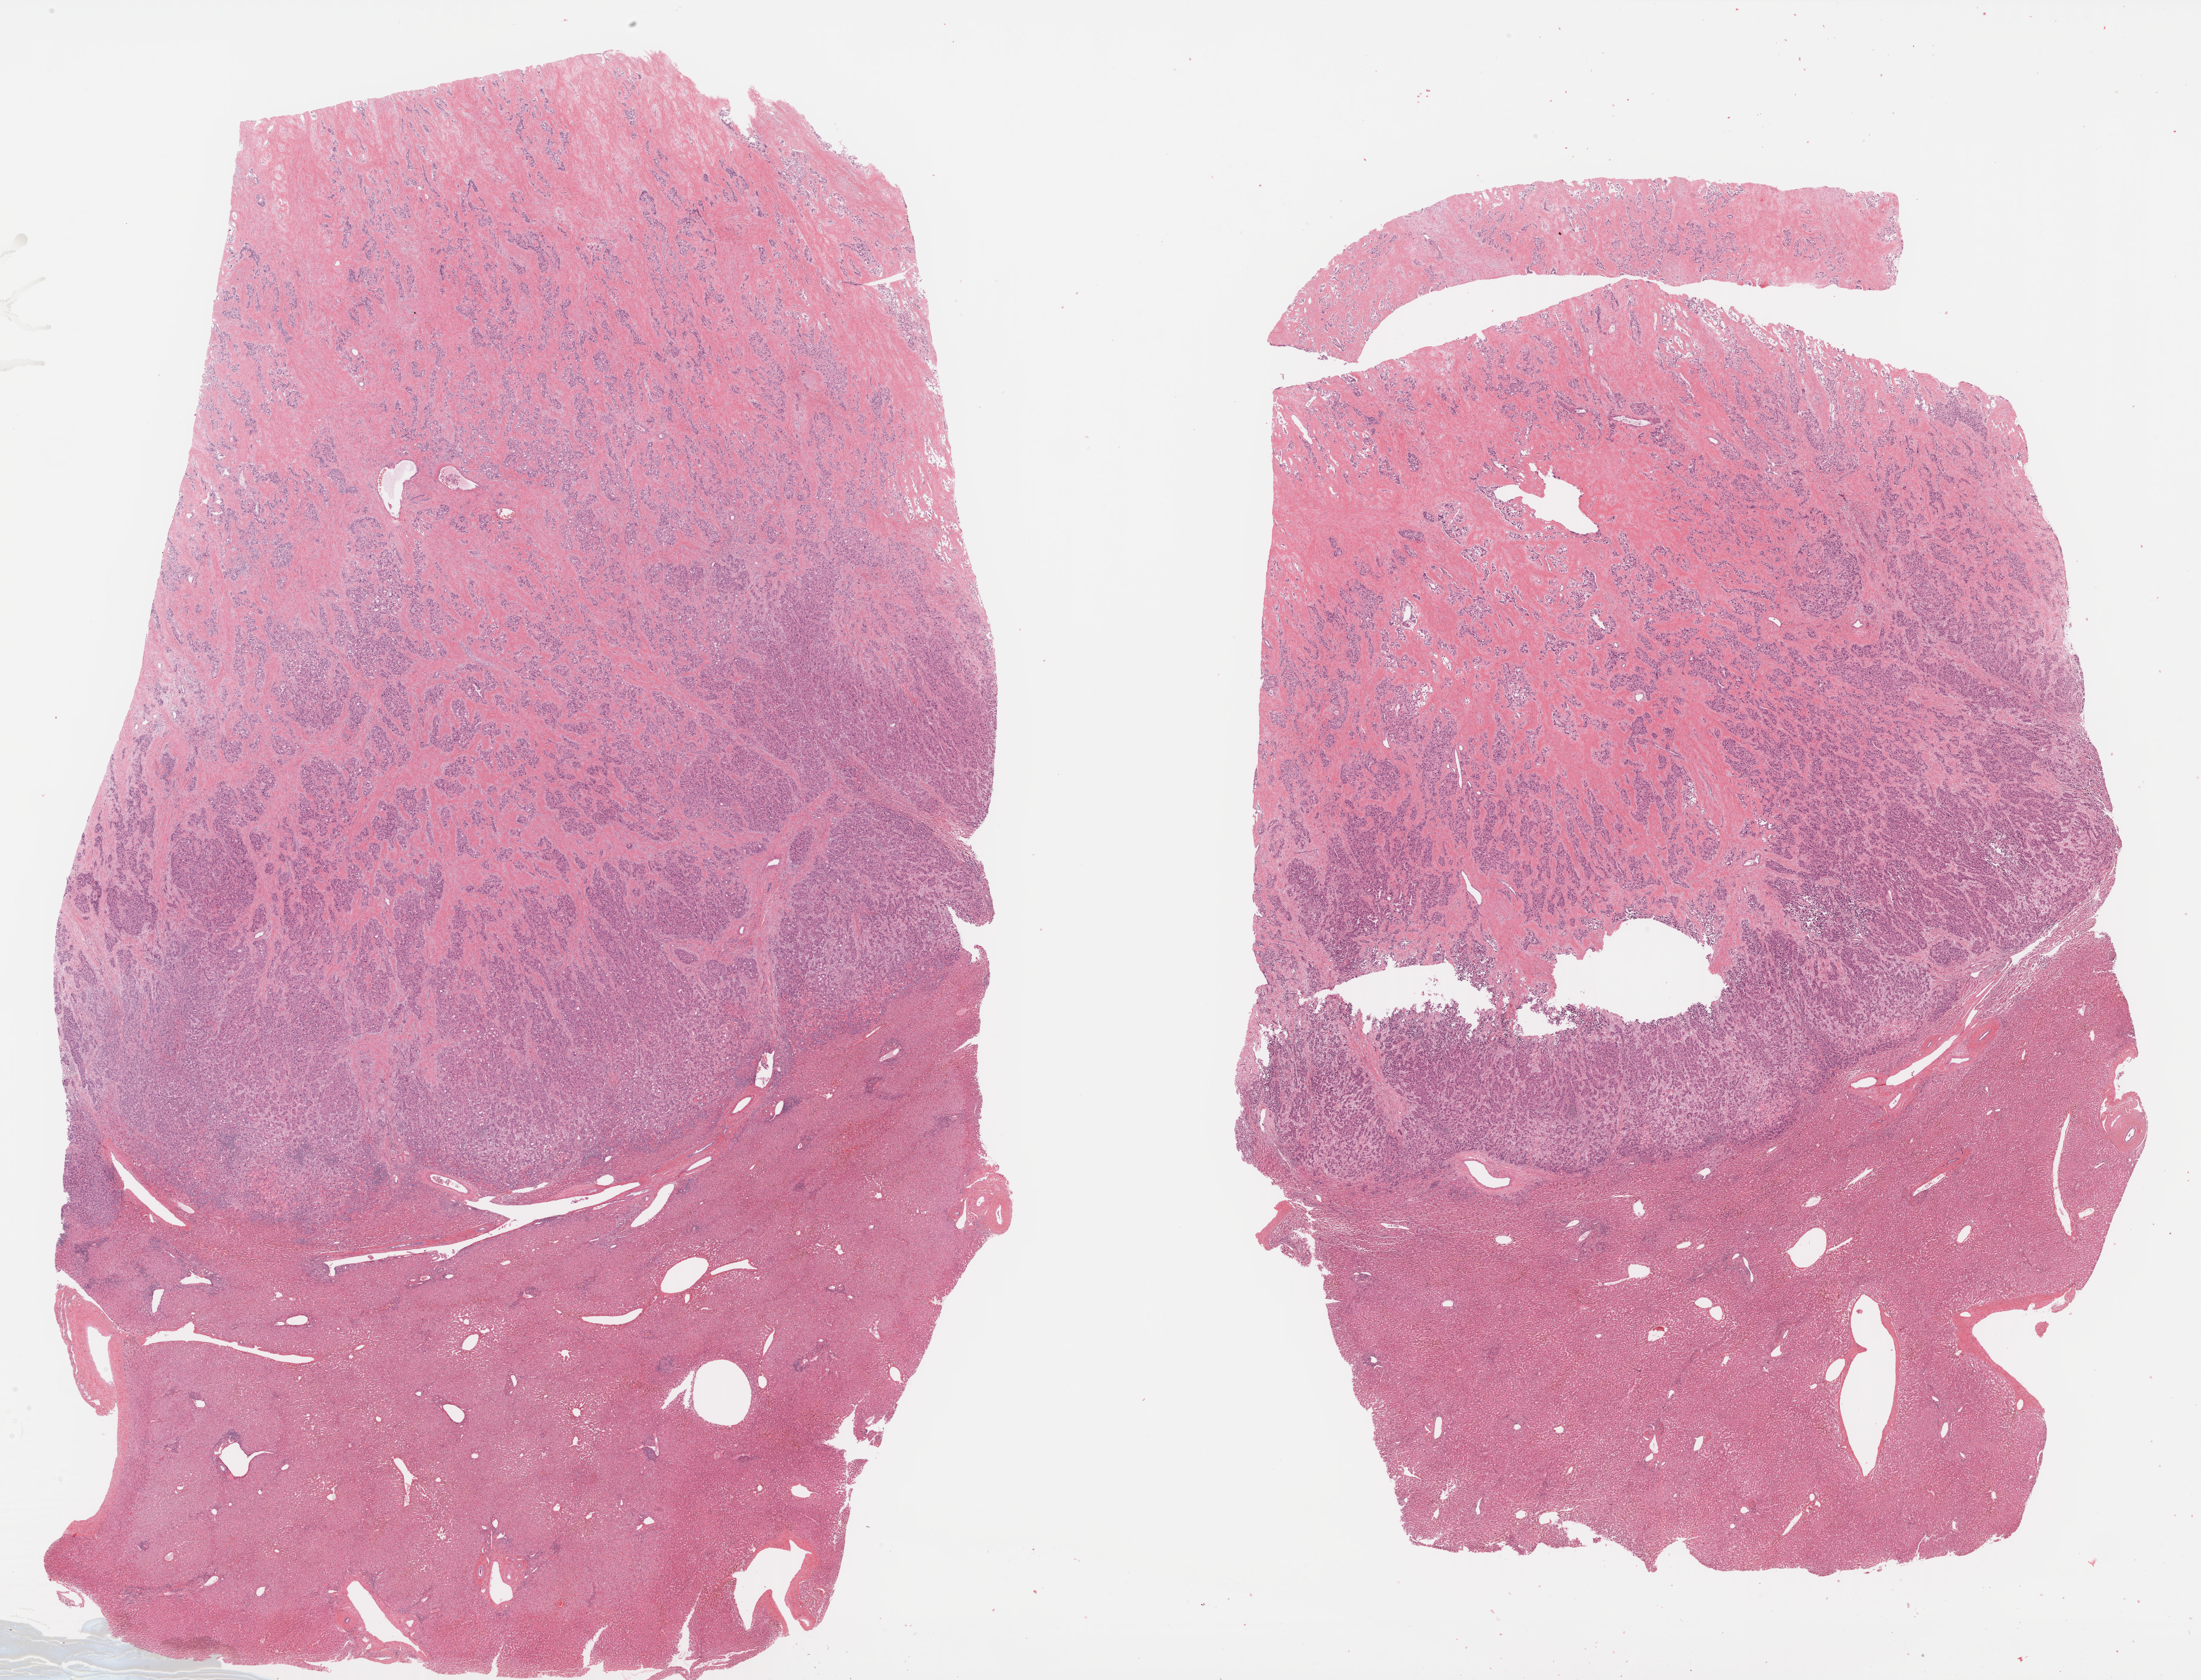
Digitized H&E-stained tissue section (whole slide), shown as a low-resolution overview of the whole scanned area (about 30.1 x 23.0 mm, acquisition: 40x scan), formalin-fixed paraffin-embedded (FFPE) diagnostic section, sample: primary tumour, liver. Female patient; age at initial diagnosis 64 years. Histologic grade: G2 (moderately differentiated).
* AJCC pathologic stage: IVB (5th edition)
* histologic diagnosis: Hepatocellular carcinoma, NOS